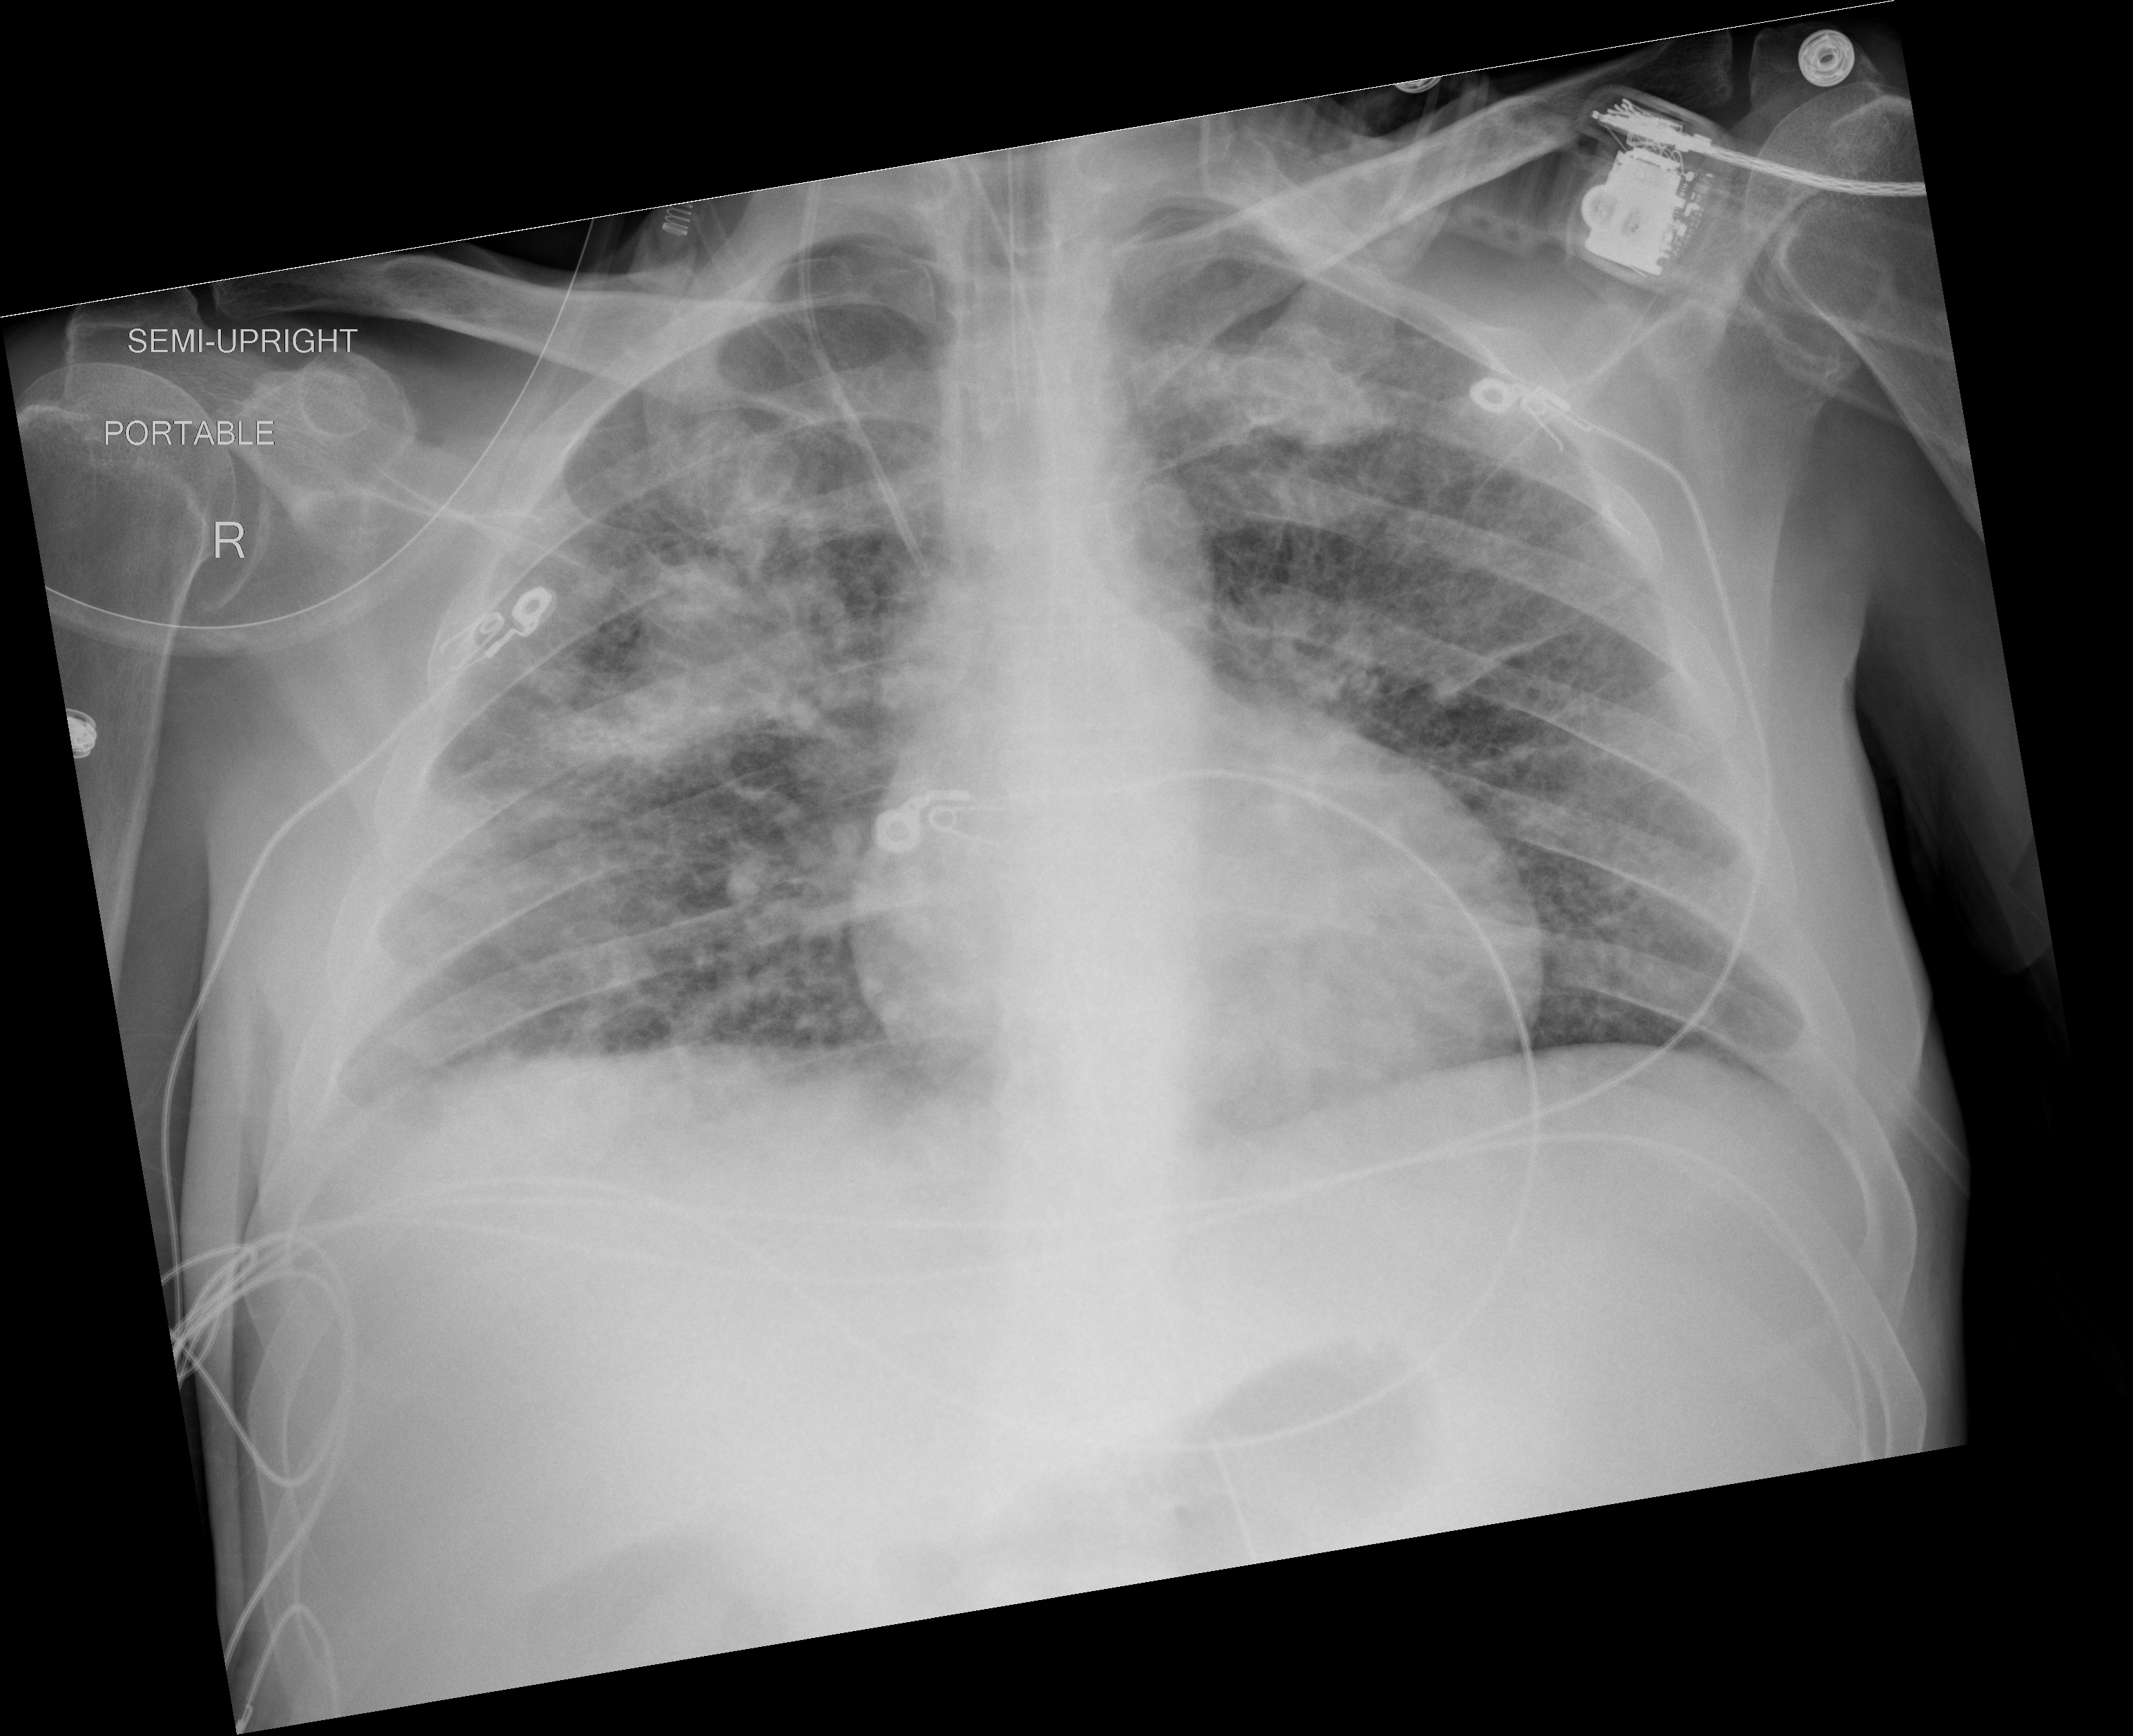
Portable chest radiograph, AP projection. Male patient, age 54 years; imaged 6 days after the COVID-19 diagnosis.
Radiologist key findings (as recorded): Persistent consolidation in the right upper lobe. Small bilateral pleural effusions.